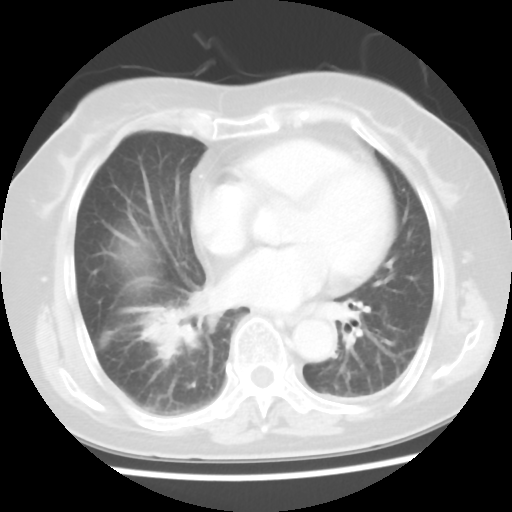
Chest CT, one axial slice; position 18 of 45 along the scan axis; reconstruction kernel STANDARD; 120 kVp; lung window (W 1500 / L -600 HU); 5 mm slice thickness; 512 × 512 image matrix. Female patient, age 65 years. From the clinical record (not read from this slice): clinical TNM (as recorded): T2 N3 M0.
Structures marked on this image (rectangle marked by the reading radiologist):
- lung tumour (recorded histology: adenocarcinoma): bounding box (x1, y1, x2, y2) in pixels: (127, 295, 201, 374)